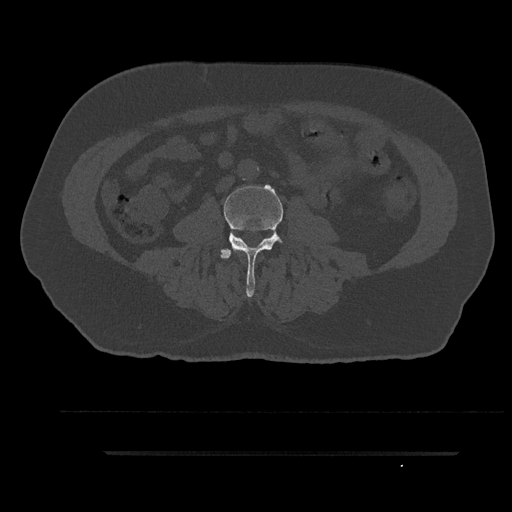
CT including the spine, one axial slice; position 34 of 797 along the scan axis; reconstruction kernel Br40s/3; bone window (W 1800 / L 400 HU); 0.5 mm slice thickness; 512 × 512 image matrix. Patient: male, 63 years. Case-level facts recorded for this patient, not image findings: primary cancer: renal; vertebrae with lytic lesions (as recorded): T8.
Annotated regions visible in this slice (semi-automatic segmentation, software-assisted and operator-edited):
- L3 vertebra: bounding box <220,185,283,297> (left, top, right, bottom; pixels)